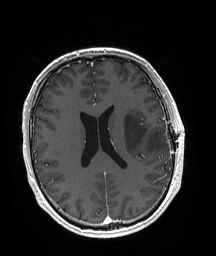
Brain MRI from a brain-tumour surgery series, one axial slice; position 81 of 192 along the scan axis; T1-weighted post-contrast; 1 mm slice thickness; 216 × 256 image matrix. Case-level facts recorded for this patient, not image findings: histopathology: Astrocytoma; WHO grade: 3; IDH mutation: yes.
Outlined on this slice (expert manual segmentation):
- tumour: box from (x=124, y=113) to (x=167, y=155) px